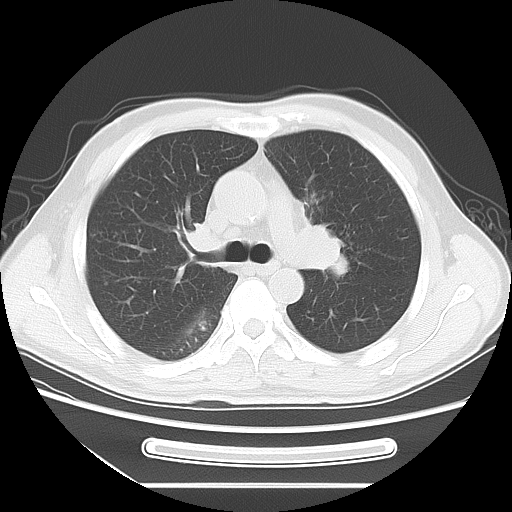
Chest CT, one axial slice. Reconstruction kernel LUNG. 120 kVp. Lung window (W 1500 / L -600 HU). 512 × 512 image matrix, field of view 366 × 366 mm. Male patient, age 51 years. From the clinical record (not read from this slice): clinical TNM (as recorded): T1c N3 M0.
Outlined on this slice (bounding box drawn by a radiologist):
- lung tumour (recorded histology: adenocarcinoma): bounding box [x1, y1, x2, y2] px = [292, 208, 353, 284]